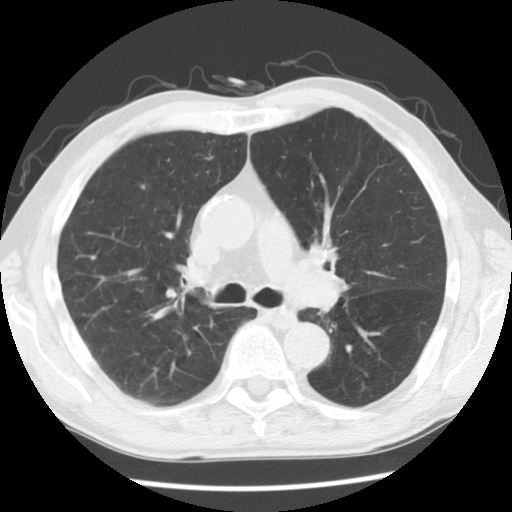
Chest CT (low-dose screening protocol), one axial image, baseline screening round, lung window (W 1500 / L -600 HU), 2.5 mm slice thickness, slice 79 of 132 in the series. Male, age 68 years at enrolment. Current smoker at enrolment.
• Lesion marked by an expert reader, bounding box [x1, y1, x2, y2] px = [293, 227, 355, 281].
• Screening reader's record for this exam: no non-calcified nodule ≥4 mm recorded.
• Later outcome: lung cancer diagnosed 215 days after this screen — squamous cell carcinoma, NOS, left hilum, stage IIB (AJCC 6th edition), 32 mm at pathology.